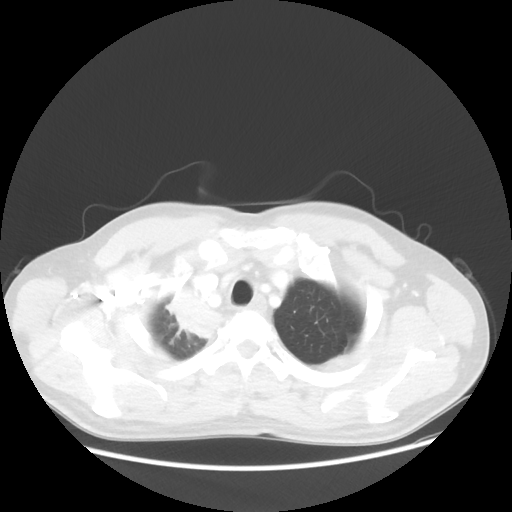
Chest CT, one axial slice; position 48 of 56 along the scan axis; 100 kVp; lung window (W 1500 / L -600 HU); 5 mm slice thickness; 512 × 512 image matrix, field of view 398 × 398 mm. Male patient, age 60 years. From the clinical record (not read from this slice): clinical TNM (as recorded): T2a N1 M0.
Outlined on this slice (rectangle marked by the reading radiologist):
- lung tumour (recorded histology: squamous cell carcinoma): bounding box [x1, y1, x2, y2] px = [159, 284, 230, 341]